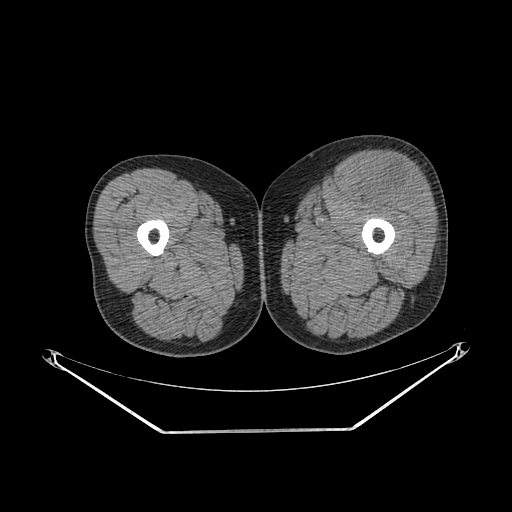
CT of an extremity soft-tissue mass (from a PET/CT study), one axial slice. Slice 229 of 267 in the series (ordered by position). Reconstruction kernel SOFT. 140 kVp. Soft-tissue window (W 400 / L 40 HU). 3.75 mm slice thickness. 512 × 512 image matrix, field of view 500 × 500 mm. Male patient. Case-level facts recorded for this patient, not image findings: histological type: extraskeletal osteosarcoma; grade: high; site of the primary tumour: thigh.
Structures marked on this image (expert contour drawn on MRI and transferred to this co-registered scan by the dataset authors):
- gross tumour volume (mass): bounding box [x1, y1, x2, y2] px = [361, 162, 426, 209]